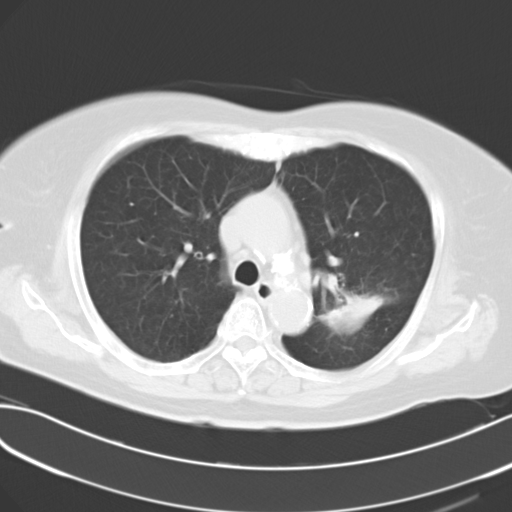
Chest CT, one axial slice; position 24 of 30 along the scan axis; reconstruction kernel B40f; lung window (W 1500 / L -600 HU); 10 mm slice thickness; 512 × 512 image matrix, field of view 353 × 353 mm. Patient: female, 70 years. Case-level facts recorded for this patient, not image findings: clinical TNM (as recorded): T2 N0 M0.
Outlined on this slice (rectangle marked by the reading radiologist):
- lung tumour (recorded histology: adenocarcinoma): bounding box <323,296,385,326> (left, top, right, bottom; pixels)